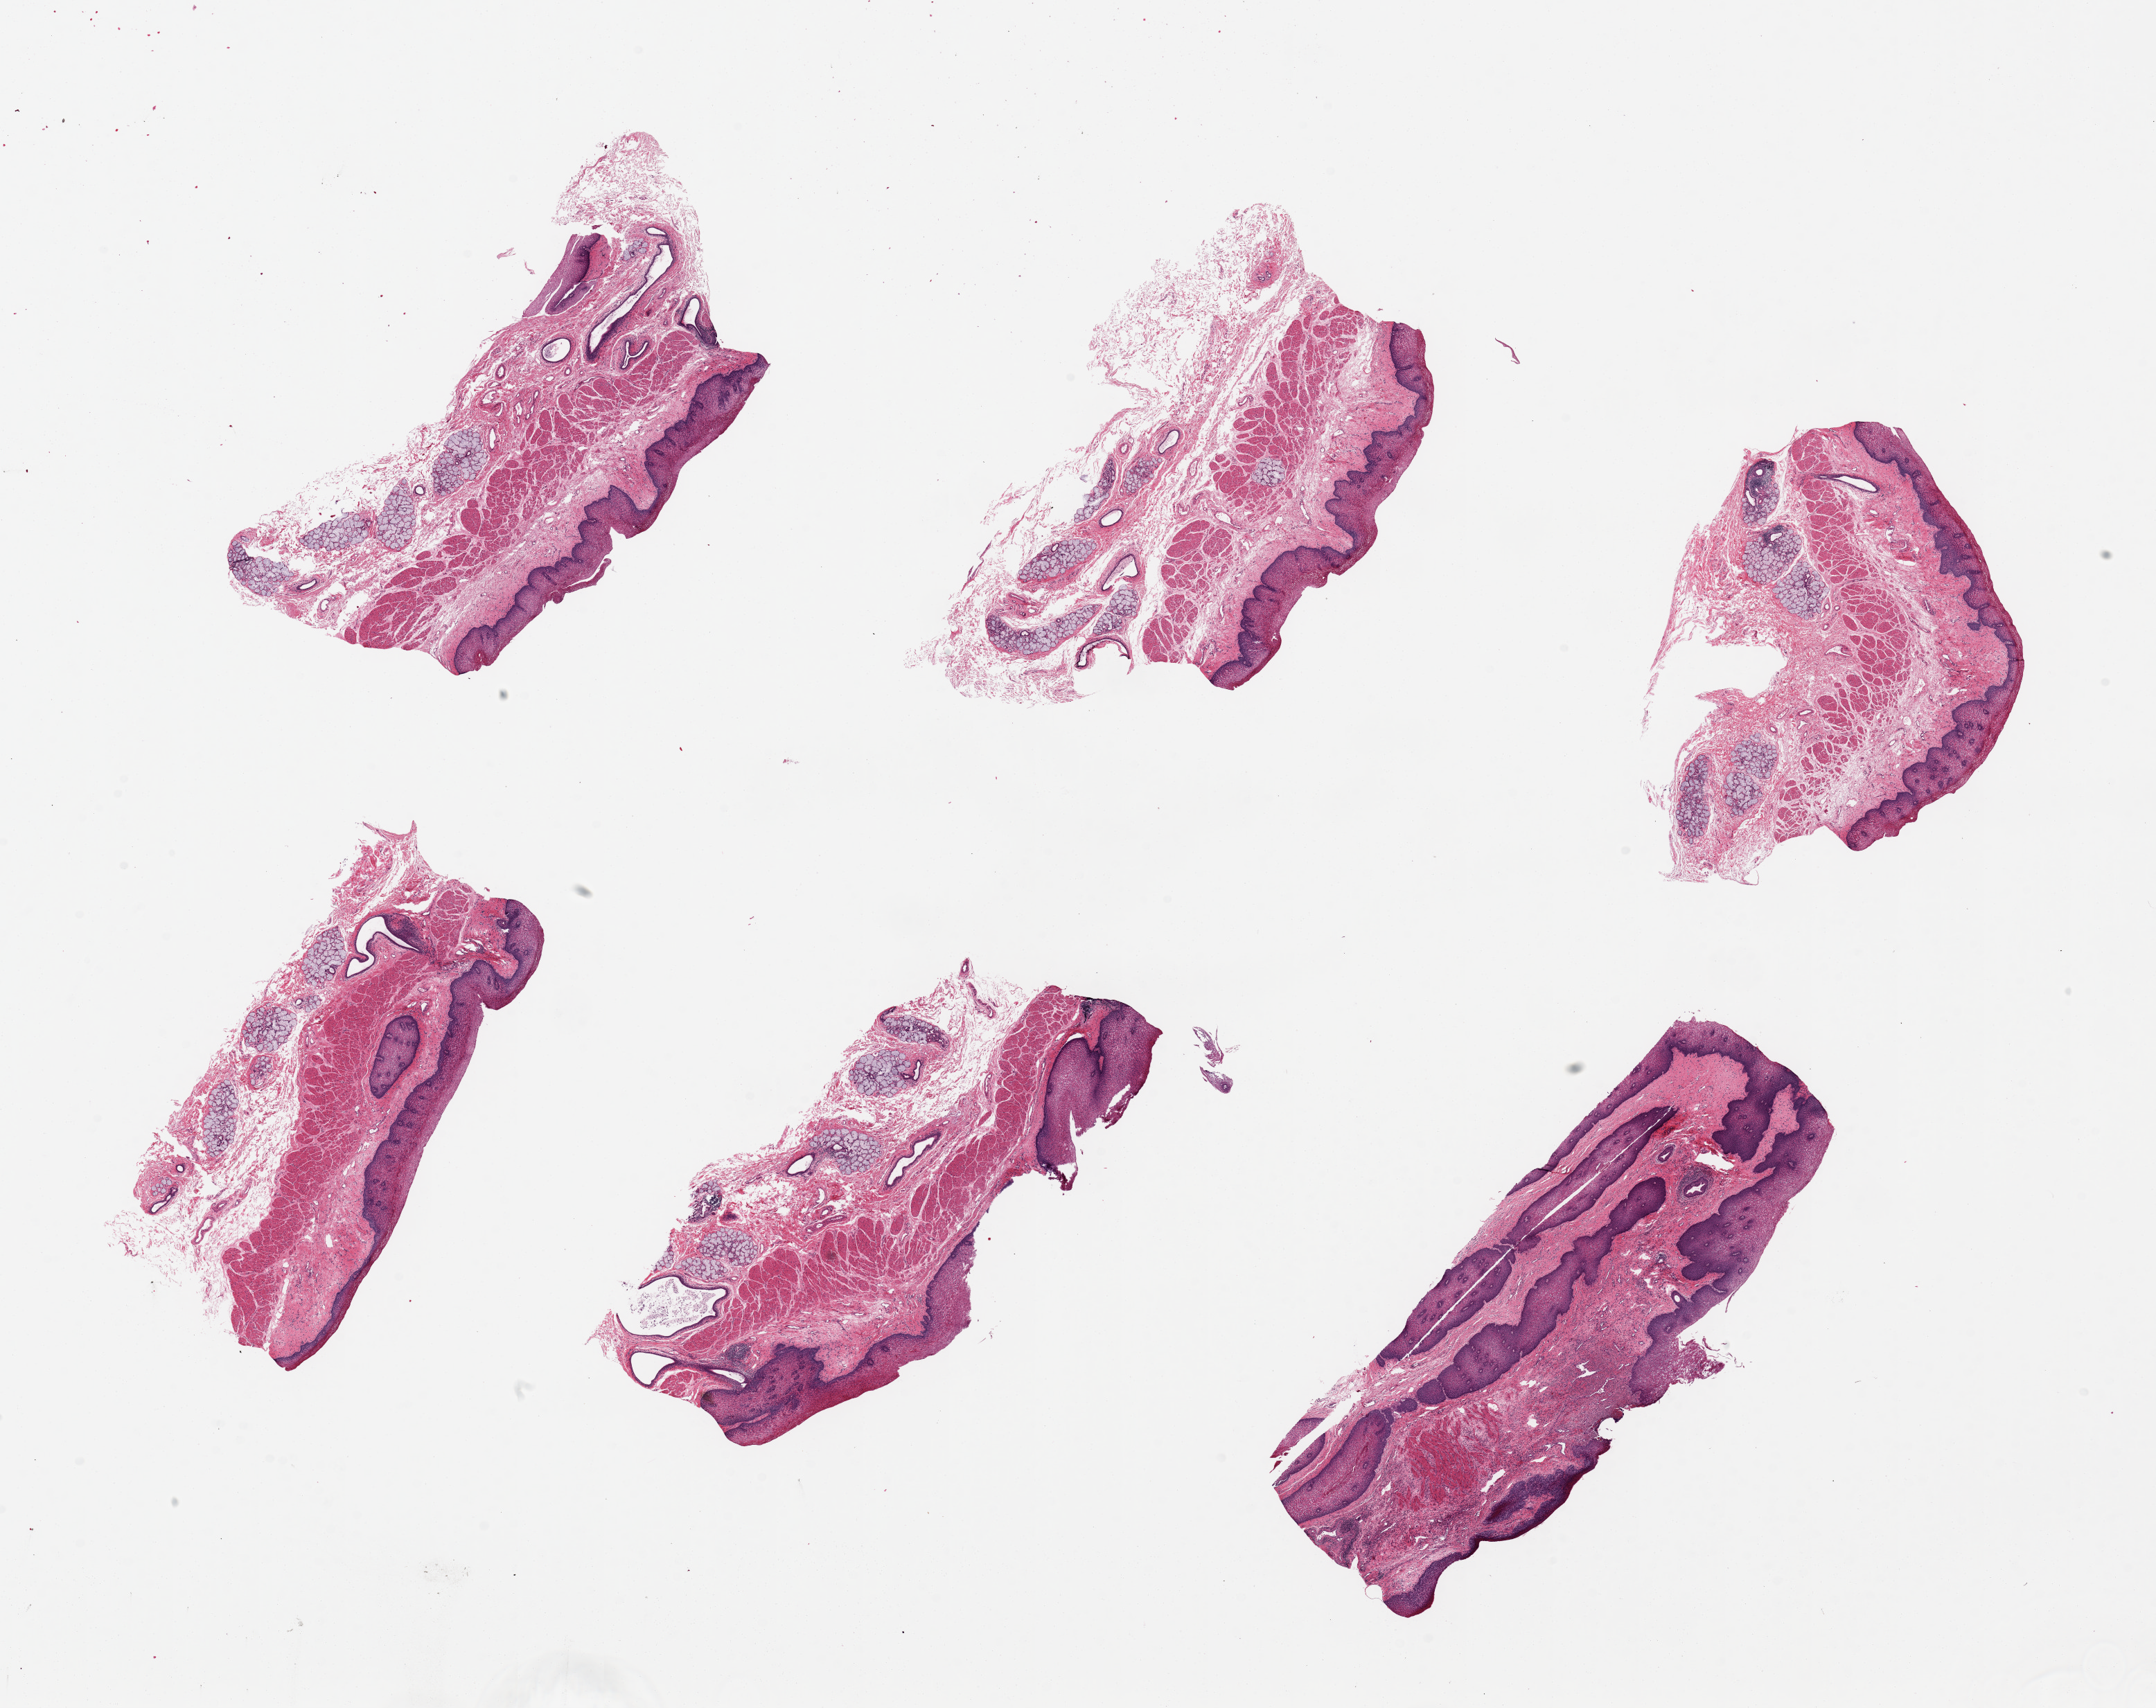
Haematoxylin and eosin whole-slide image, shown as a low-resolution overview of the whole scanned area (about 24.6 x 19.5 mm). PAXgene-fixed, paraffin-embedded tissue. Section of esophageal mucous membrane (target tissue). Tissue donor sample. Donor sex: female.
- reviewer comment on this tissue sample: 6 pieces up to 8x2 mm; largest piece has an ulcer with acute inflammation